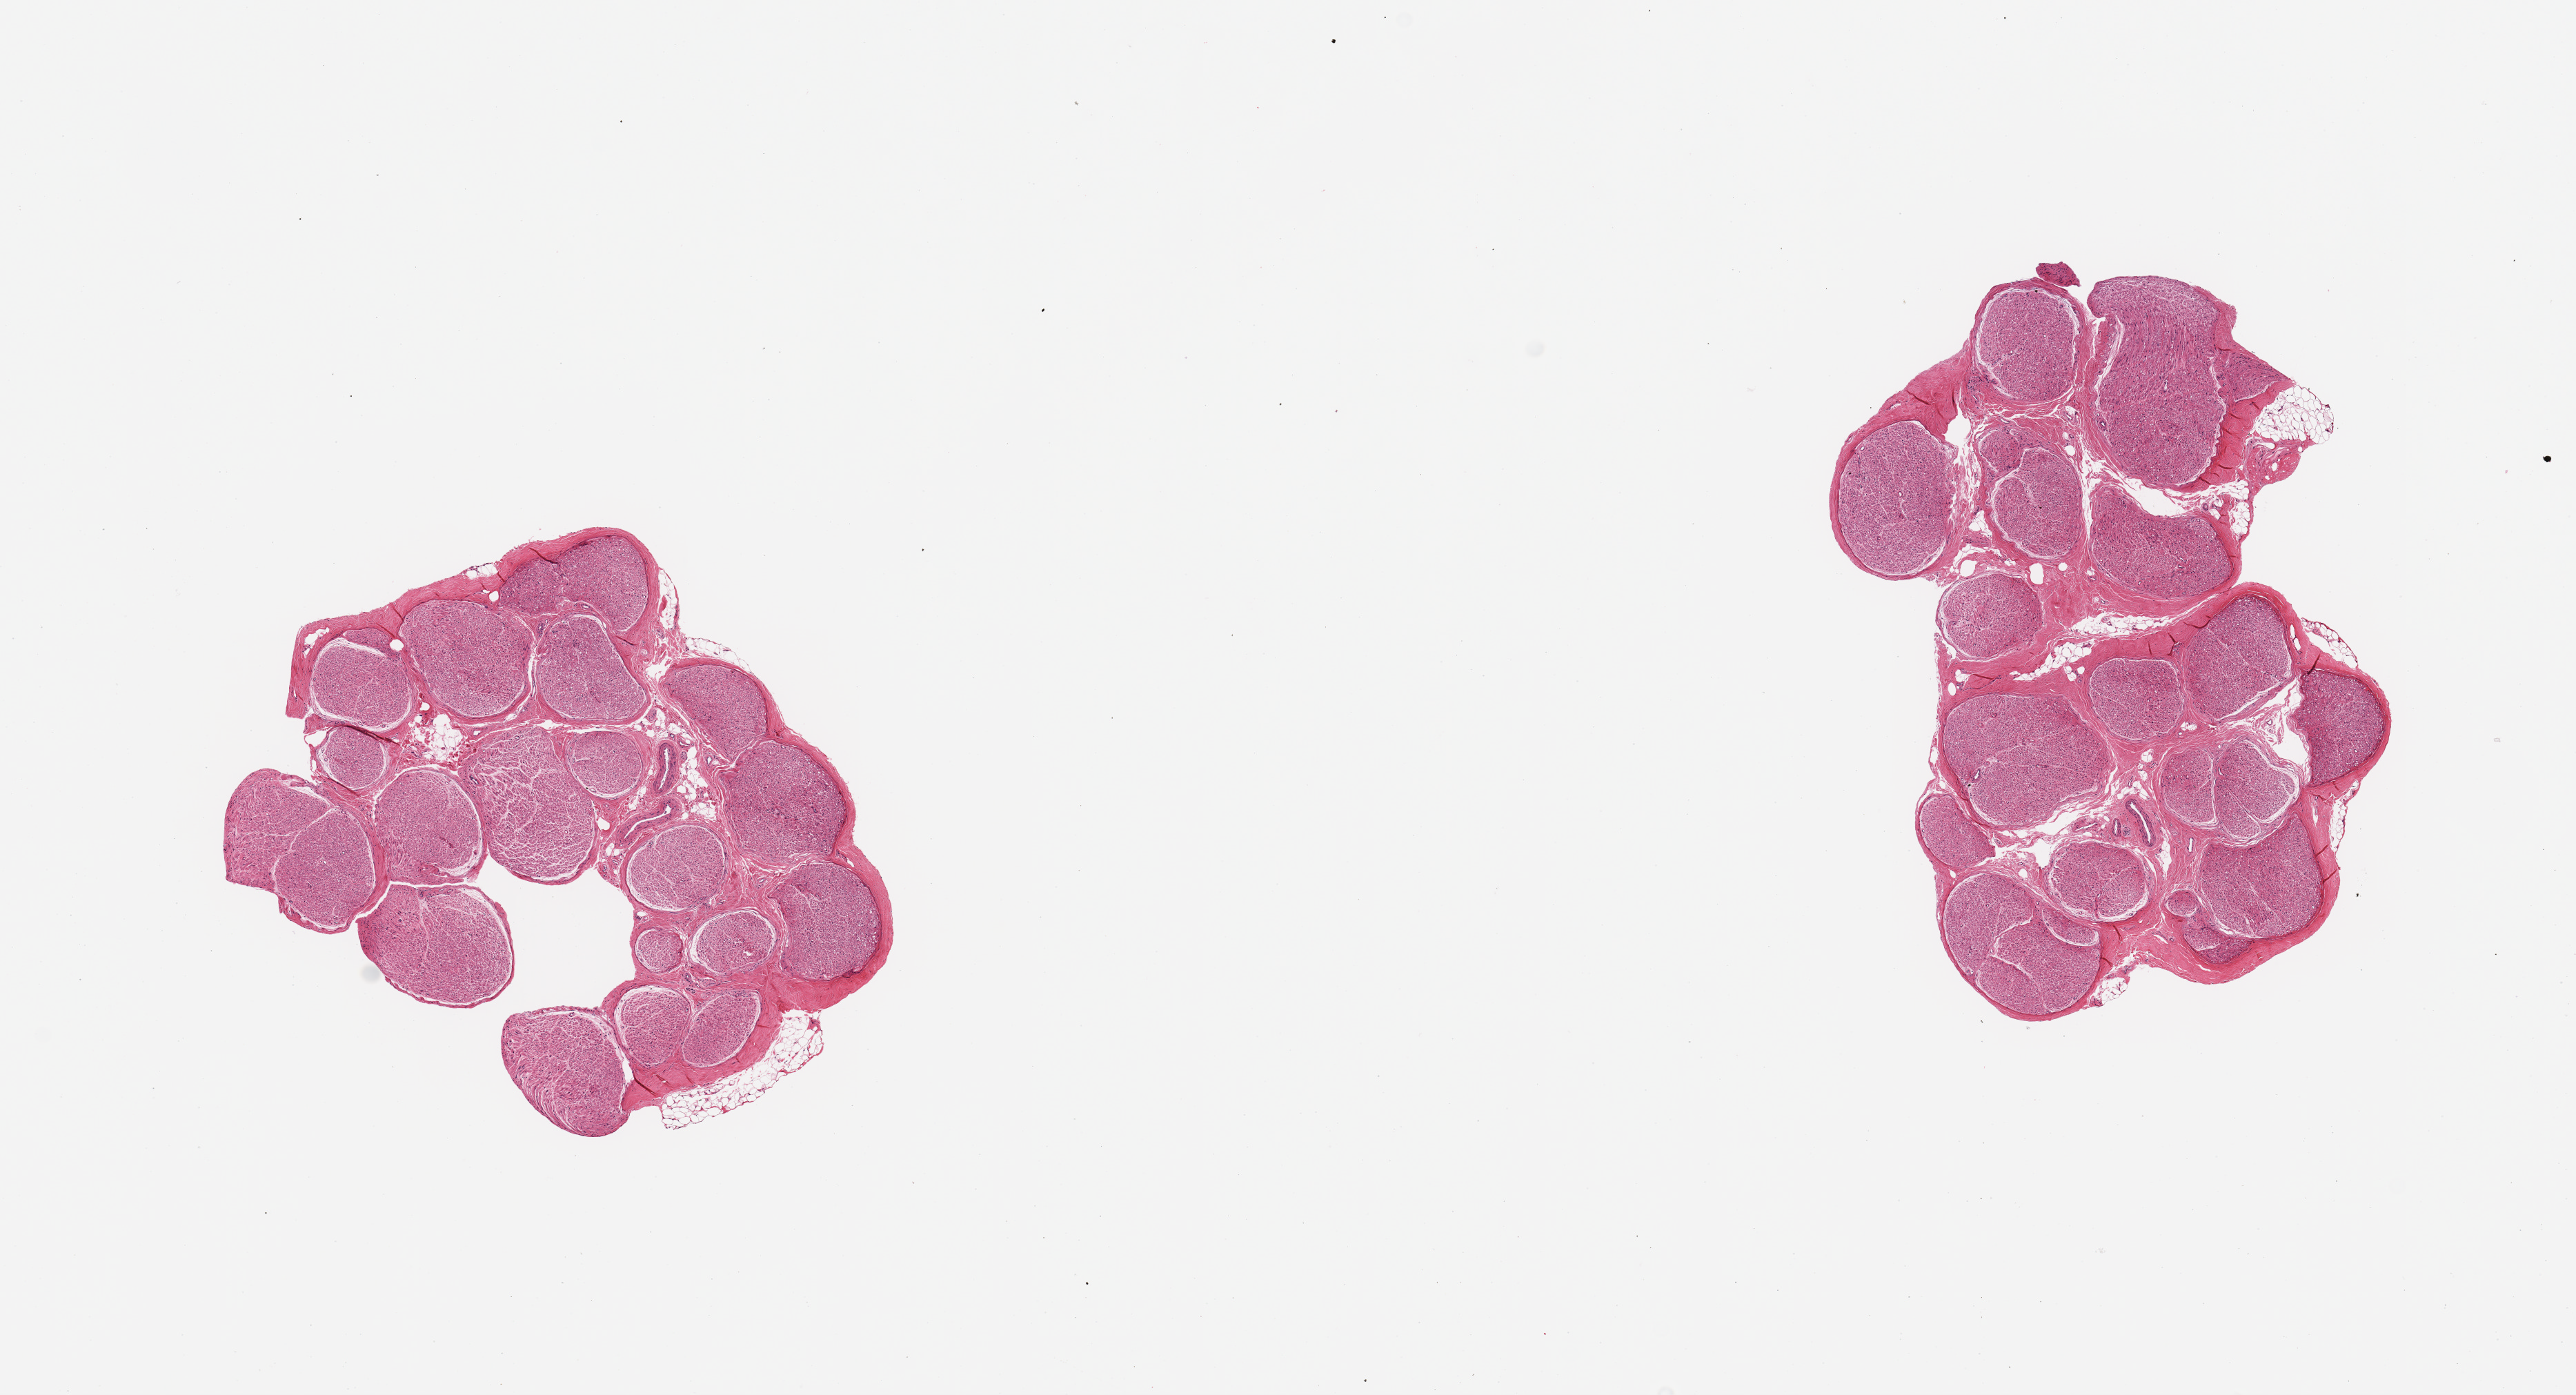
Digitized haematoxylin and eosin-stained section, a low-resolution overview of the entire scanned area, about 14.8 x 8.0 mm (slide scanned at 20x); PAXgene-fixed paraffin-embedded (PFPE) section; section of tibial nerve (target tissue); donor tissue sample. Male donor.
Pathologist's review note for this sample: 2 pieces; well trimmed; 5% internal and external fat.